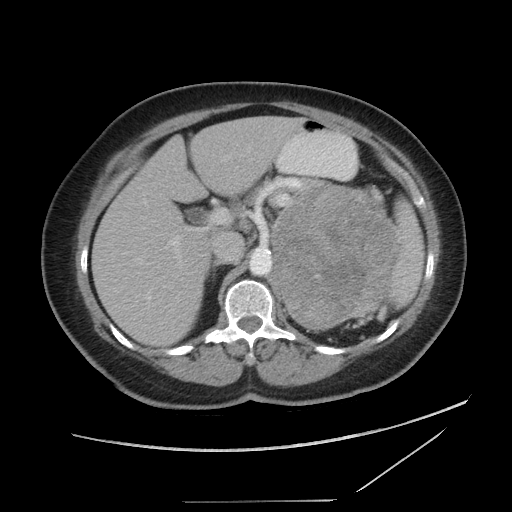
Contrast-enhanced abdominal CT, one axial slice; reconstruction kernel STANDARD; 120 kVp; soft-tissue window (W 400 / L 40 HU); 5 mm slice thickness; 512 × 512 image matrix, field of view 398 × 398 mm. Female patient, age 77 years. From the clinical record (not read from this slice): diagnosis: adrenocortical carcinoma; tumour side: left adrenal; tumour size at pathology: 13.1 cm; Ki-67 index: 10 %; stage (as recorded): 3.
Annotated regions visible in this slice (semi-automatically segmented with operator editing):
- mass: box from (x=273, y=187) to (x=397, y=328) px